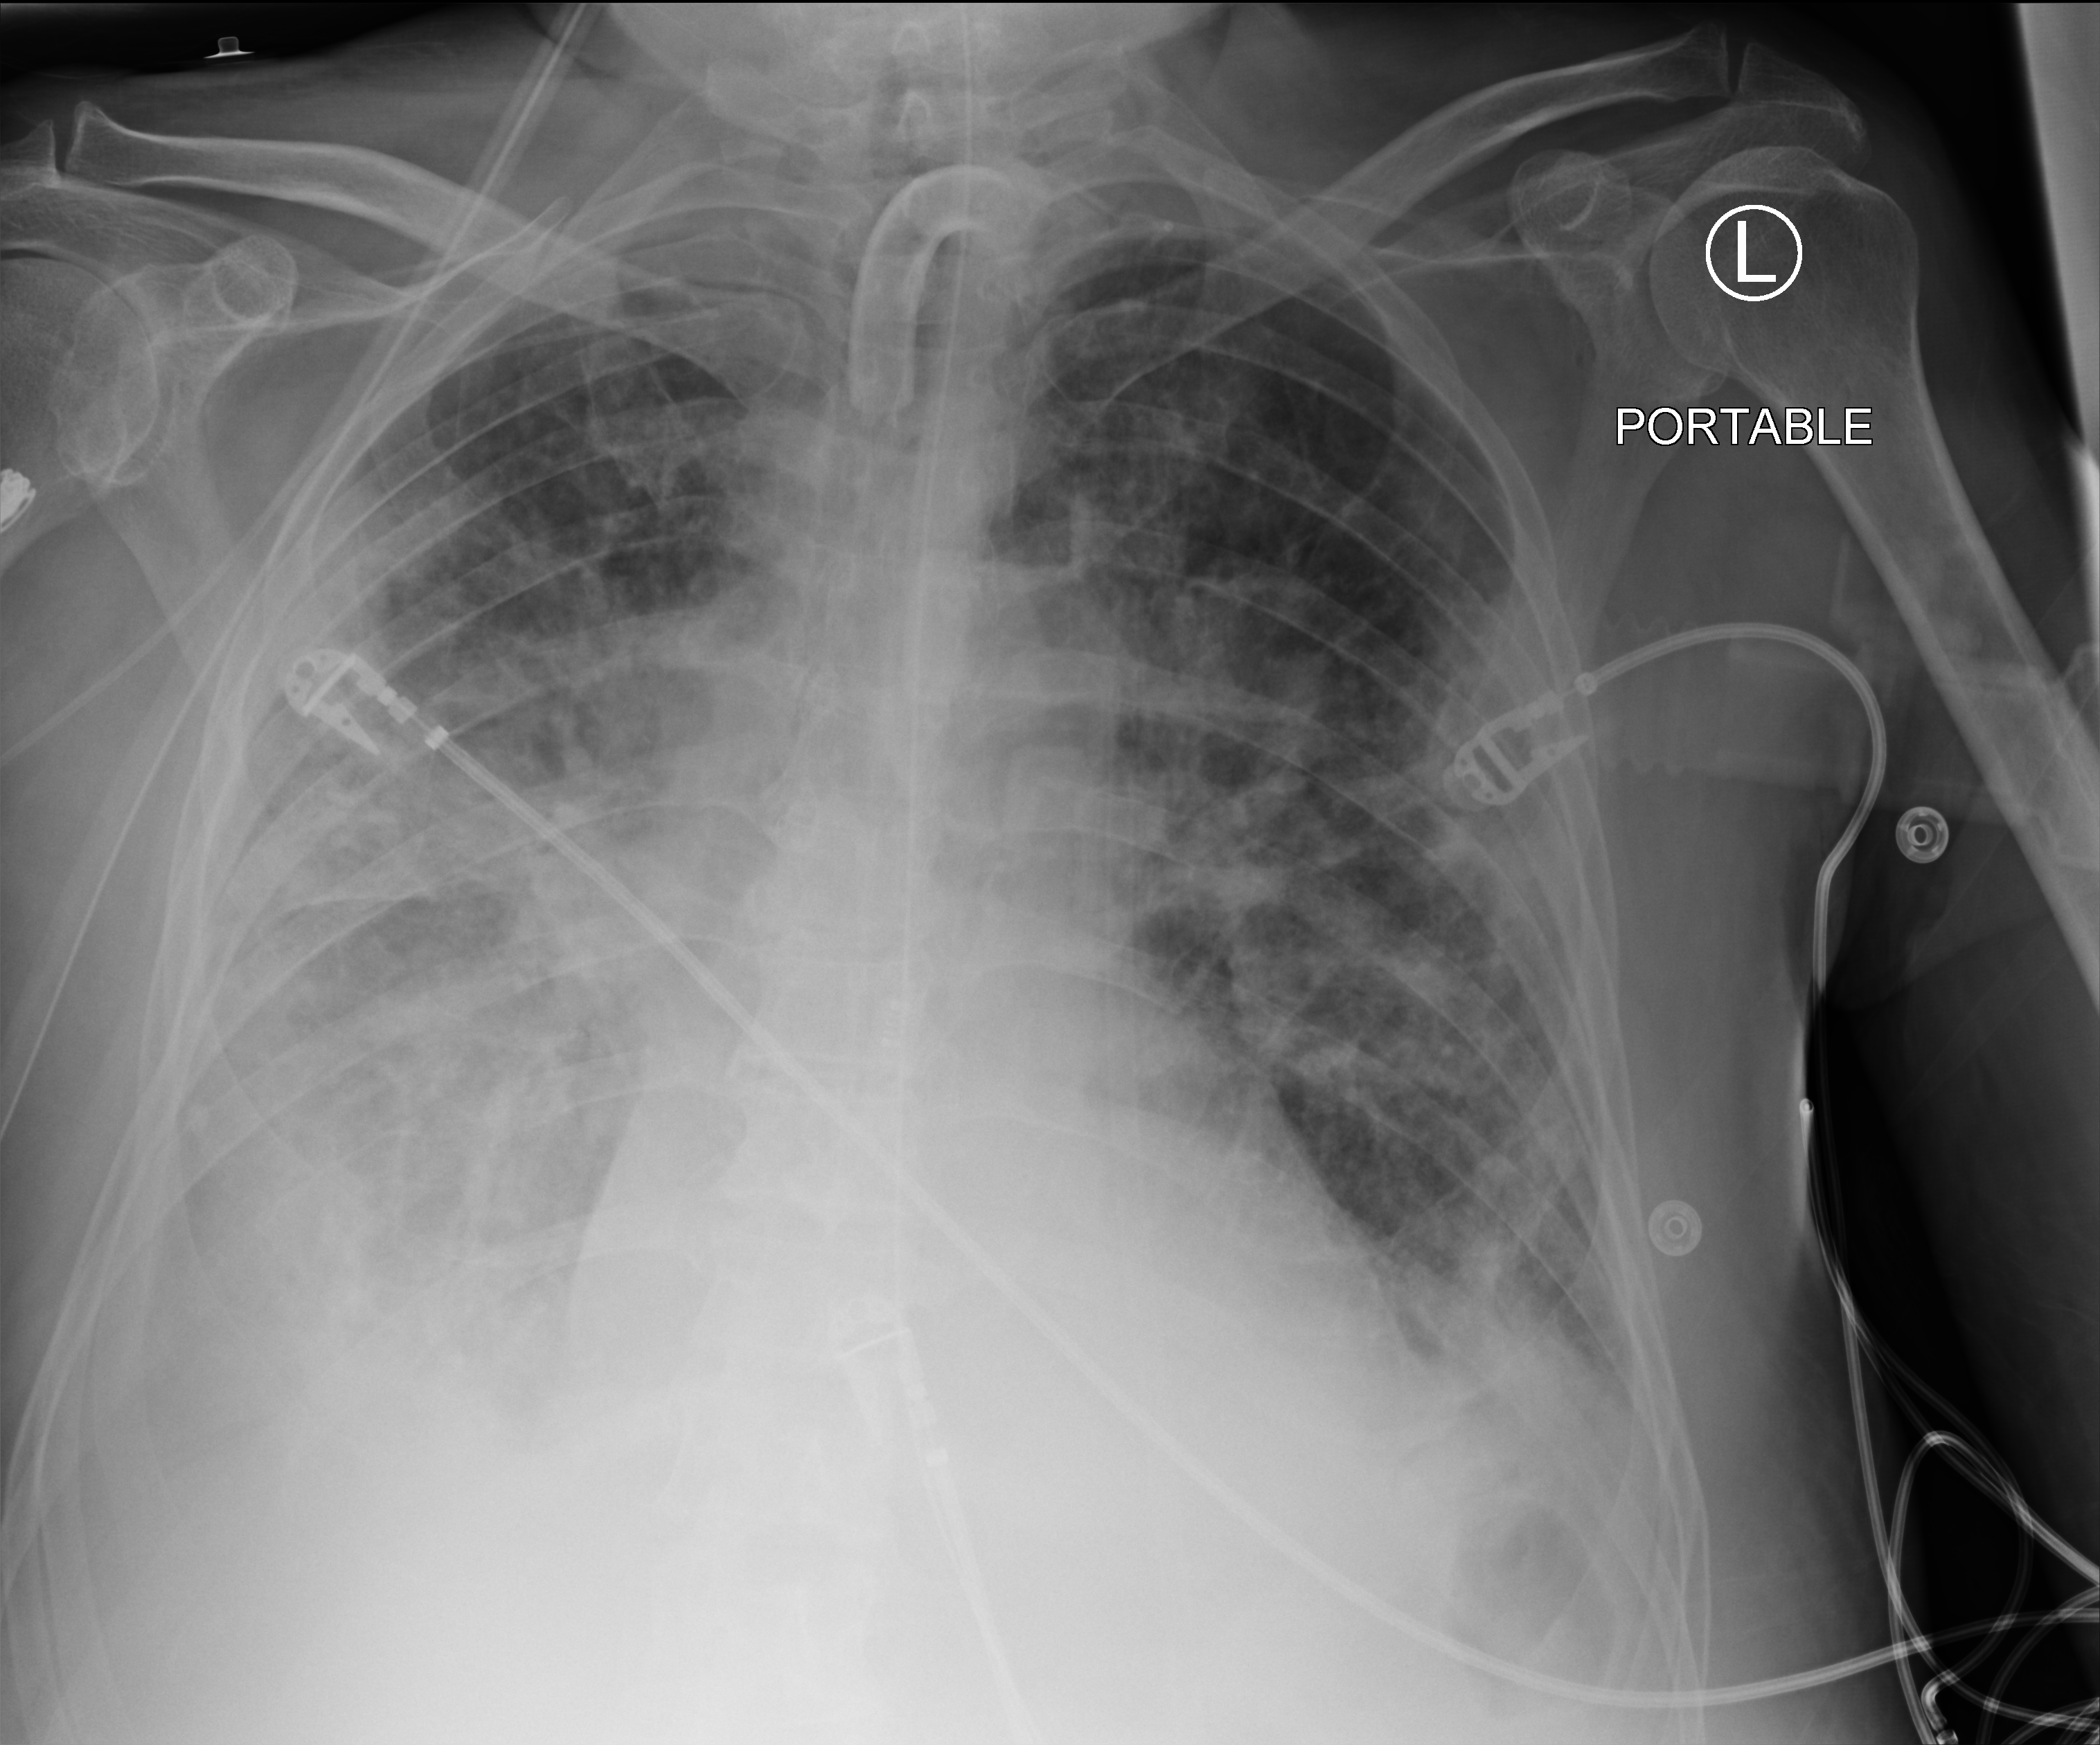
Chest X-ray (portable); anteroposterior (AP) projection. Patient hospitalised with COVID-19; male, aged 75–90 years.
Hospital-stay facts (about this admission, not read from this image; timing relative to this image not recorded):
- mechanically ventilated during this hospital stay: yes